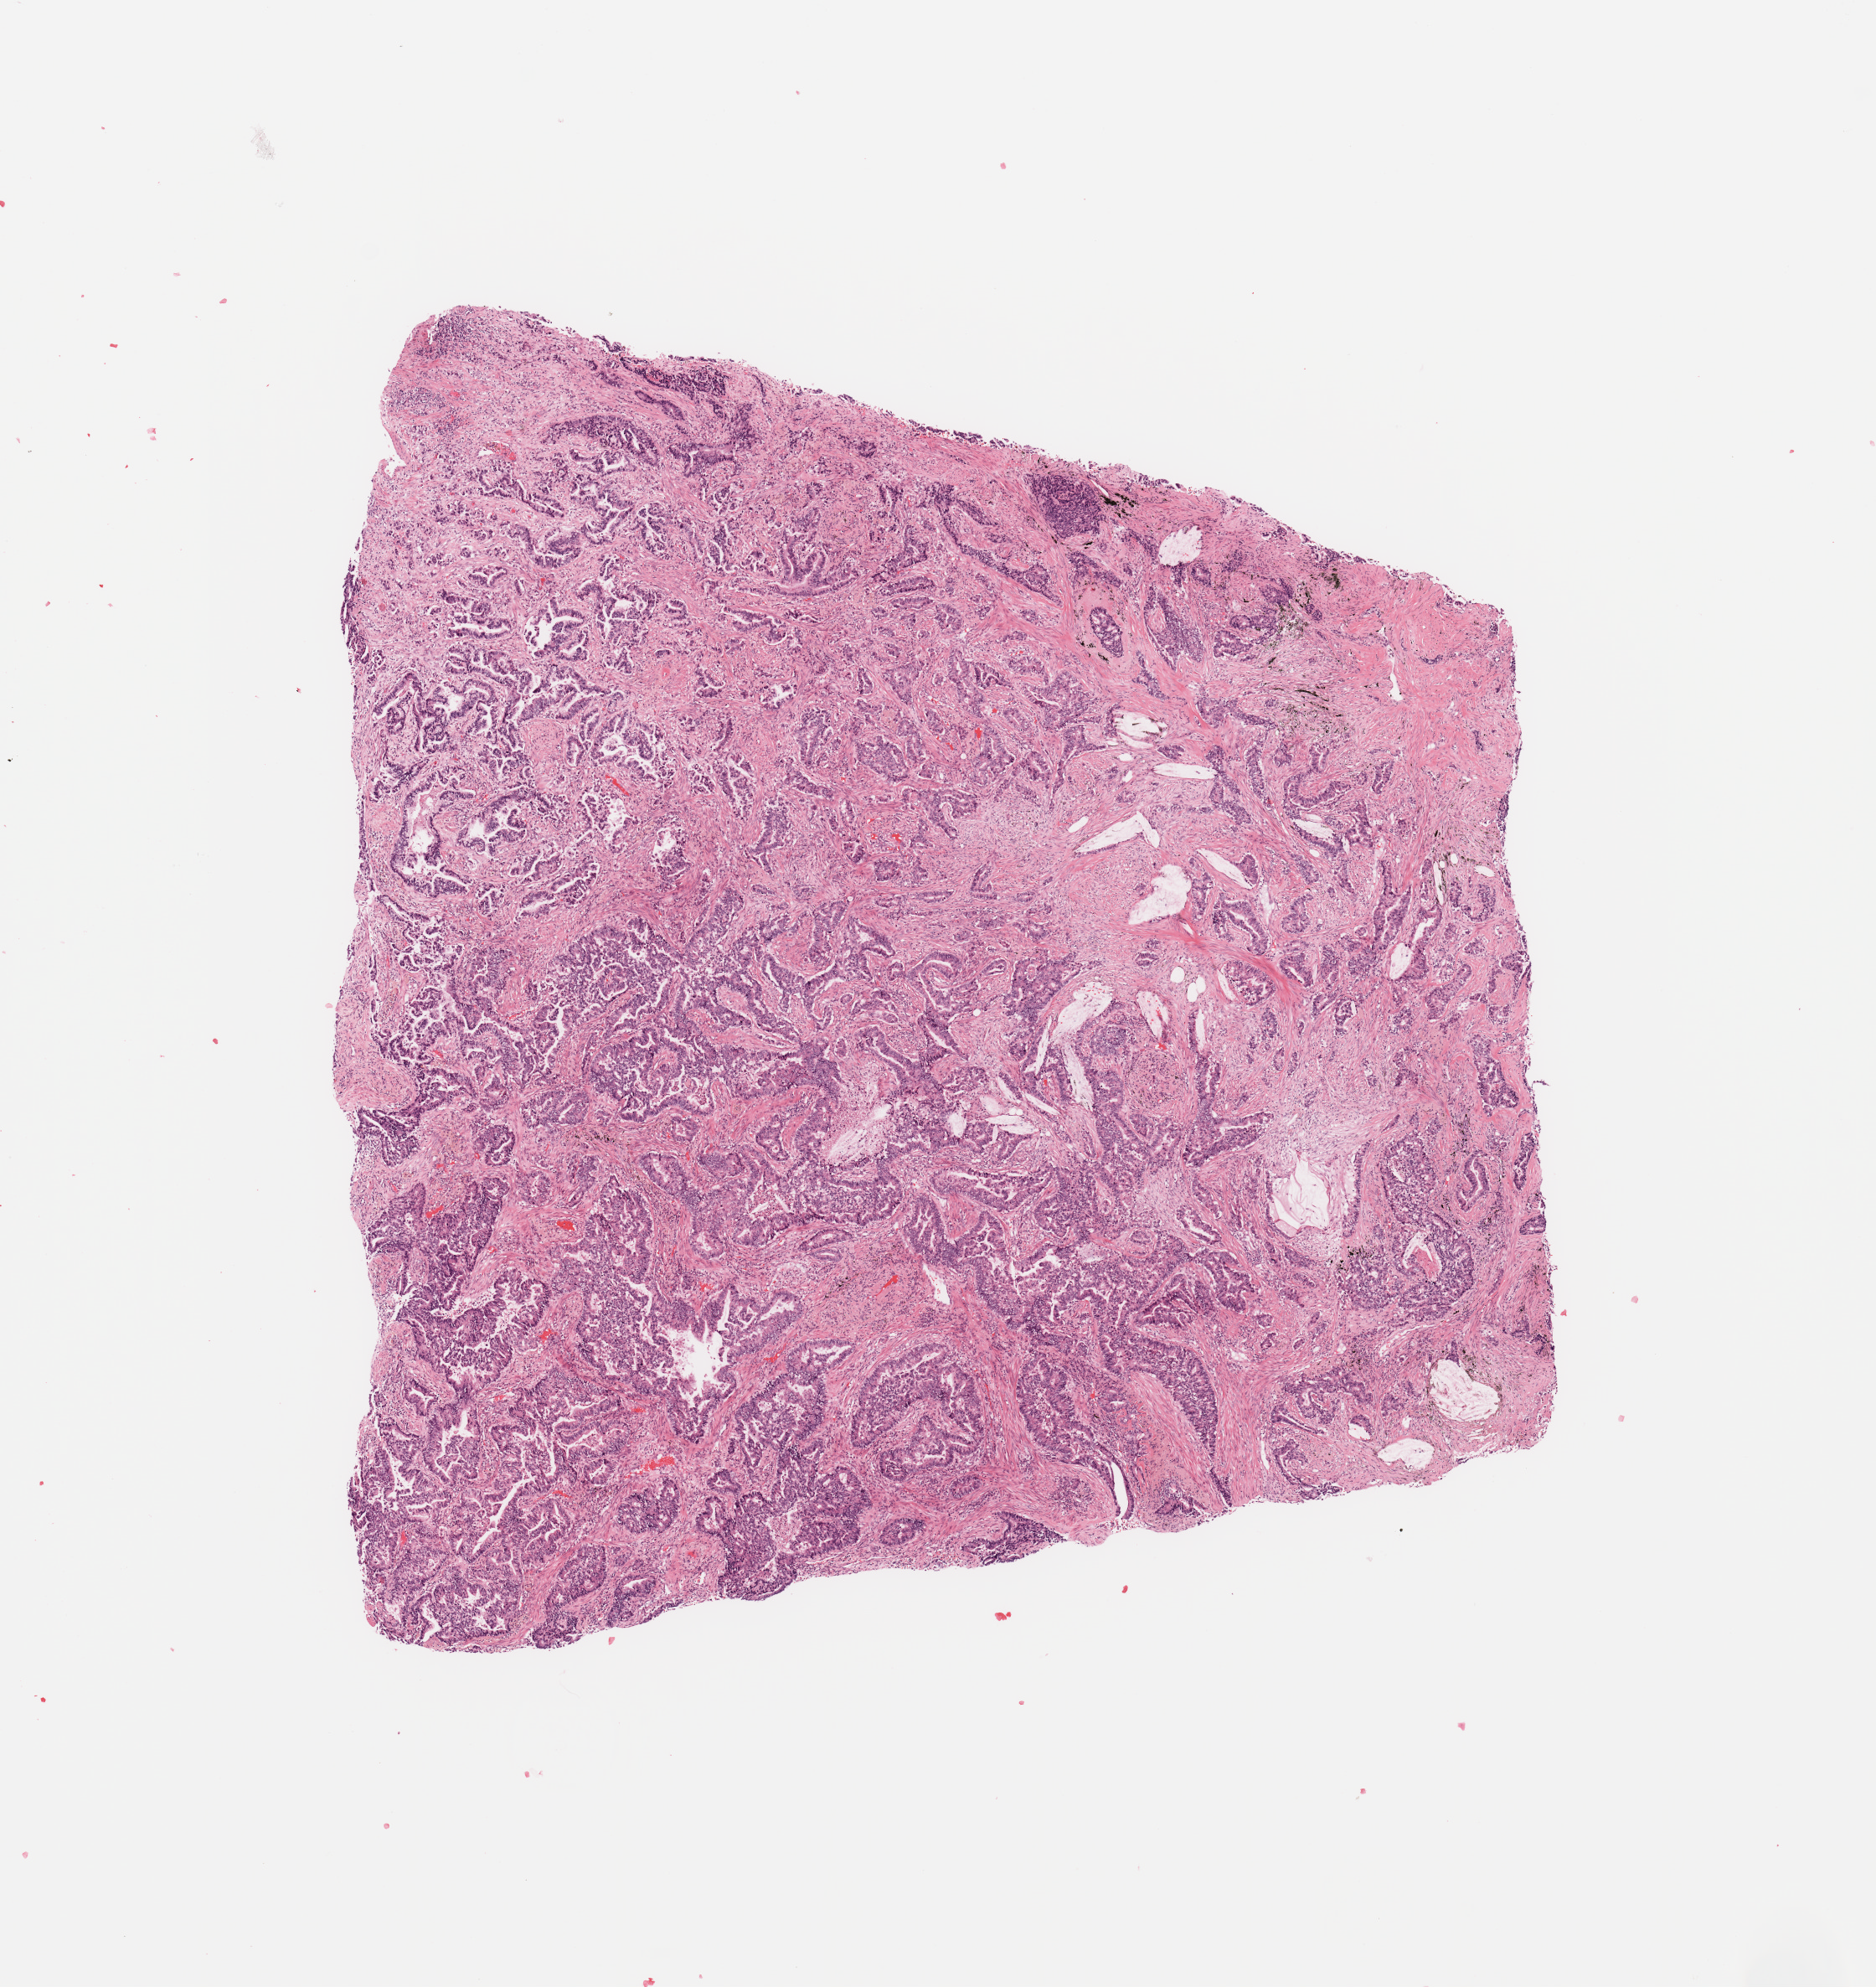
H&E whole-slide image, a low-resolution overview of the entire scanned area, about 8.9 x 9.4 mm (acquisition: 20x scan); tumour tissue sample, sampled site: lung. Female, 59 y/o. Histologic grade: G2 (moderately differentiated). Slide review estimates, as recorded: tumour nuclei 70%, necrosis 5%.
Histologic diagnosis: Adenocarcinoma, NOS. AJCC pathologic stage: IB. Primary tumour site (as recorded): left upper lobe.